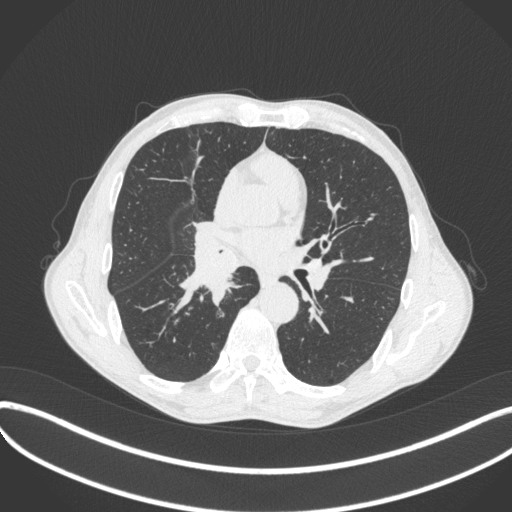
Chest CT, one axial slice. Slice 229 of 481 in the series (ordered by position). Reconstruction kernel B31f. Lung window (W 1500 / L -600 HU). 1 mm slice thickness. 512 × 512 image matrix, field of view 400 × 400 mm. Male patient, age 65 years. Case-level facts recorded for this patient, not image findings: clinical TNM (as recorded): T2a N0 M0; histopathological grade: G2.
Annotated regions visible in this slice (rectangle marked by the reading radiologist):
- lung tumour (recorded histology: squamous cell carcinoma): bounding box <176,235,242,314> (left, top, right, bottom; pixels)